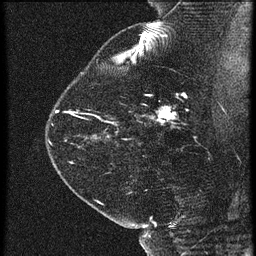
Breast MRI (dynamic contrast-enhanced), one sagittal slice. Position 45 of 60 along the scan axis. 3 images stored at this slice position (order not interpretable as contrast timing). 1.5 T. TE 4.2 ms, TR 21.3 ms. 256 × 256 image matrix. Female patient, age 42 years. From the clinical record (not read from this slice): setting: breast cancer imaged before/during neoadjuvant chemotherapy; receptor status: HER2-positive.
Structures marked on this image (semi-automatically segmented with operator editing):
- analysis volume of interest (the breast-tissue region the enhancement analysis was run in; not a lesion): bounding box [x1, y1, x2, y2] px = [122, 82, 195, 147]
- tumour enhancement mask (voxels above the 90 % enhancement threshold inside the analysis volume of interest): [152, 106, 176, 123]